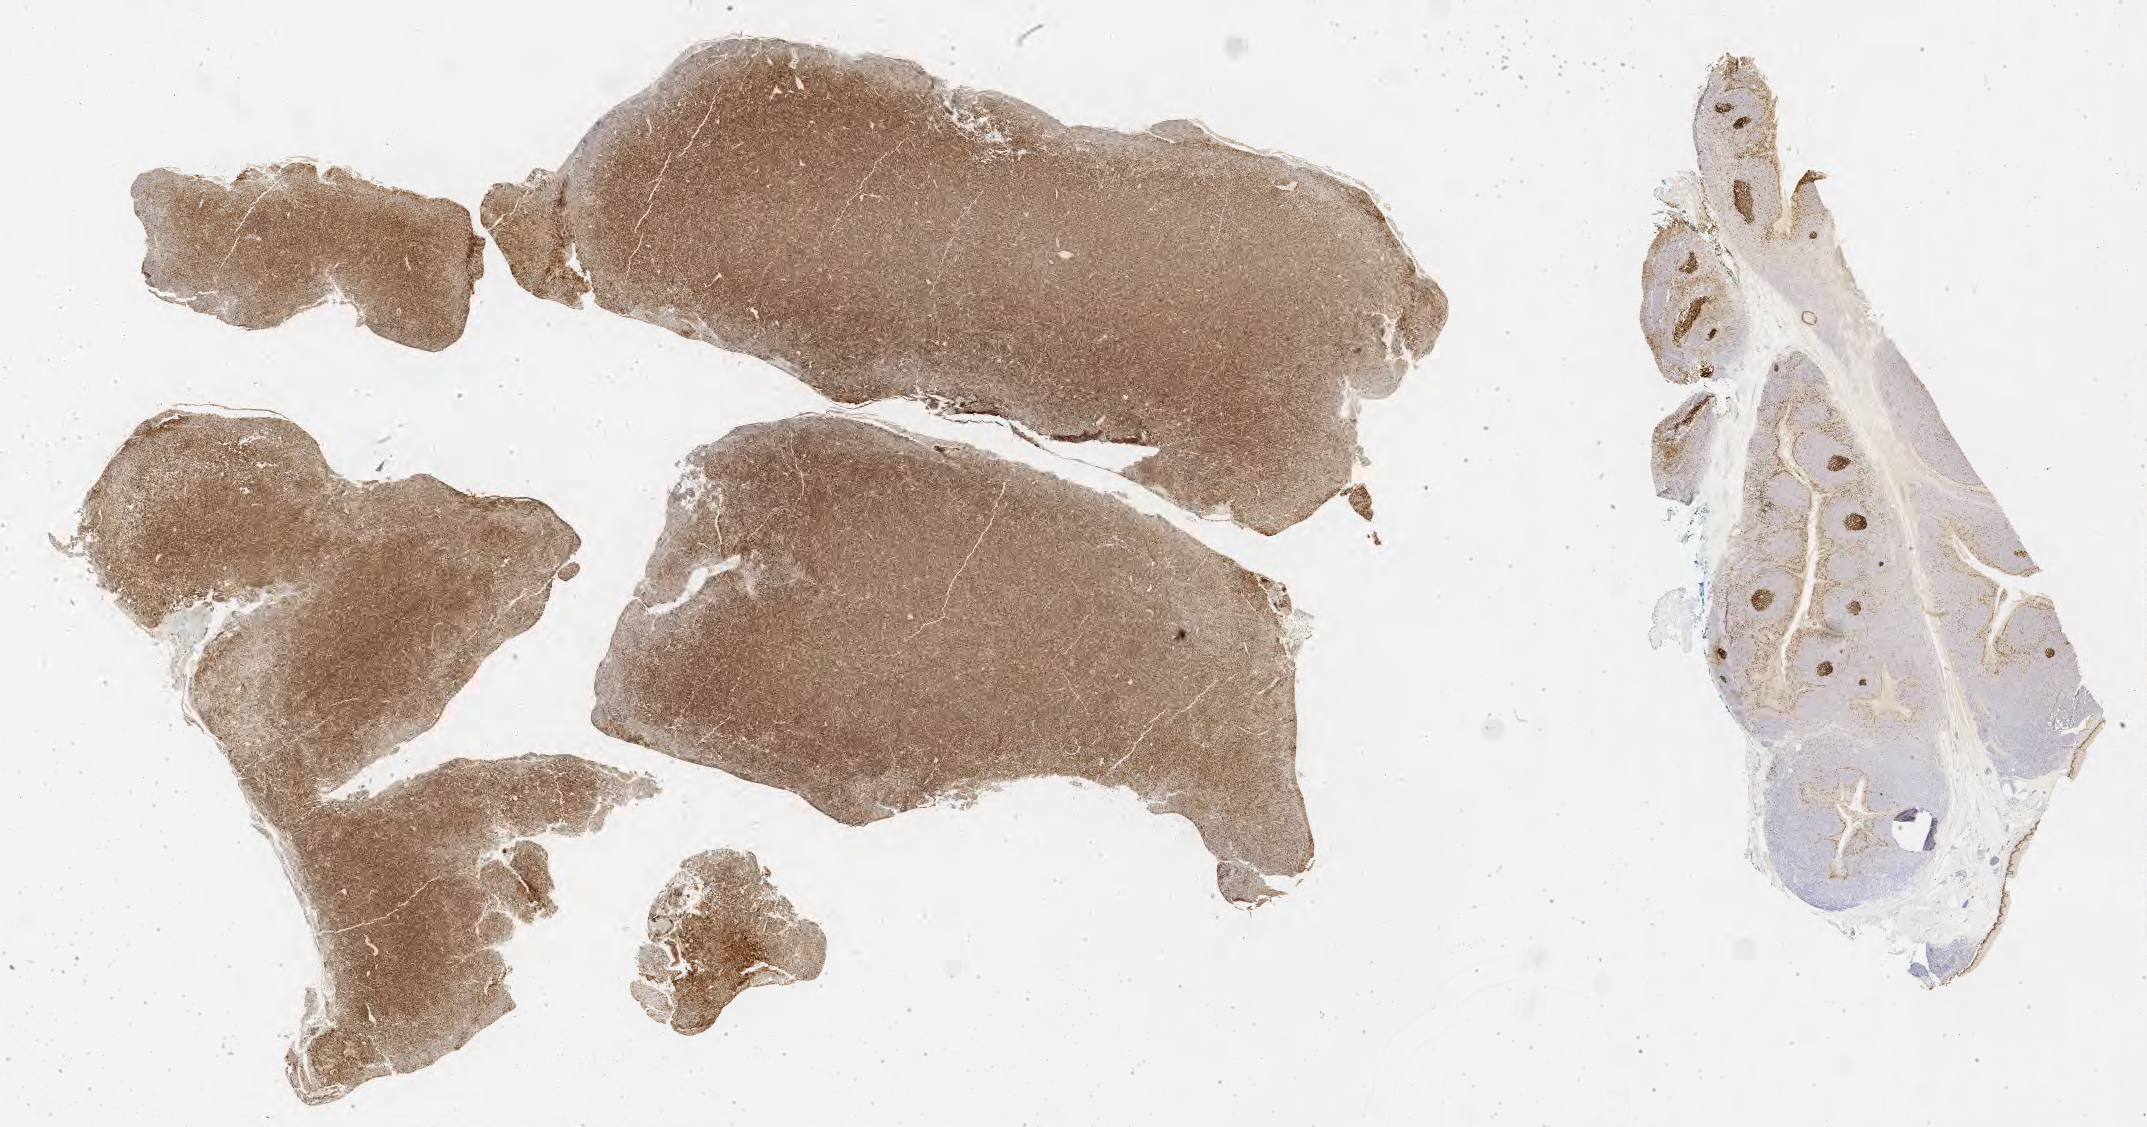
IHC for Ki-67, whole-slide image — whole scanned area (about 34.7 x 18.2 mm) shown as a low-resolution overview. Specimen: tumor tissue. Site: peritoneum. Patient: female, age at initial diagnosis 7 years.
• histologic diagnosis: Burkitt lymphoma, NOS